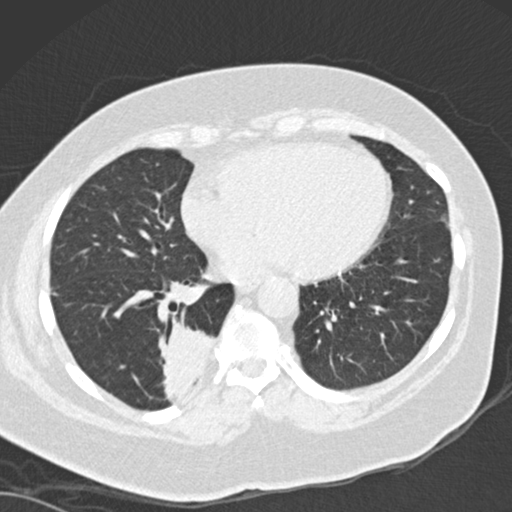
Chest CT (low-dose screening protocol), one axial image. Baseline screening round. Lung window (W 1500 / L -600 HU). 2 mm slice thickness. Slice 101 of 162 in the series. Female, age 66 years at enrolment. Current smoker at enrolment.
• Expert-annotated lung lesion, box from (x=147, y=317) to (x=230, y=403) px.
• The screening reader recorded 3 non-calcified nodules or masses ≥4 mm on this exam; which of them this box marks is not recorded.
• Official screen result: positive, change unspecified: nodule(s) >= 4 mm or enlarging nodule(s), mass(es), or other non-specific abnormalities suspicious for lung cancer.
• Participant outcome: lung cancer diagnosed 67 days after this screen — adenocarcinoma, NOS, right lower lobe, well differentiated (G1), stage IB (AJCC 6th edition), 55 mm at pathology.